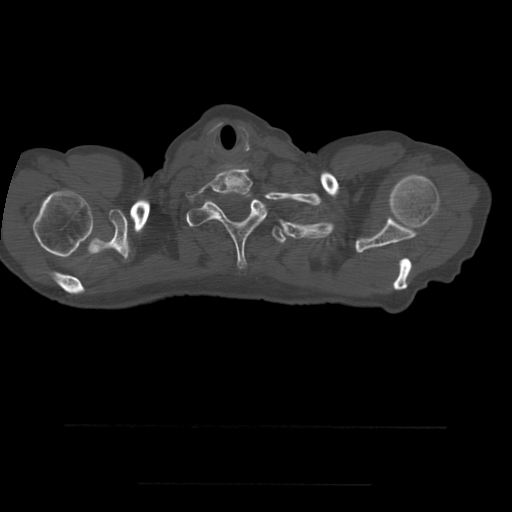
CT including the spine, one axial slice; position 448 of 544 along the scan axis; bone window (W 1800 / L 400 HU); 1.25 mm slice thickness; 512 × 512 image matrix. Patient age 58 years. Case-level facts recorded for this patient, not image findings: primary cancer: lung.
Annotated regions visible in this slice (semi-automatically segmented with operator editing):
- T1 vertebra: bounding box <187,193,268,269> (left, top, right, bottom; pixels)
- T2 vertebra: <272,227,287,244>